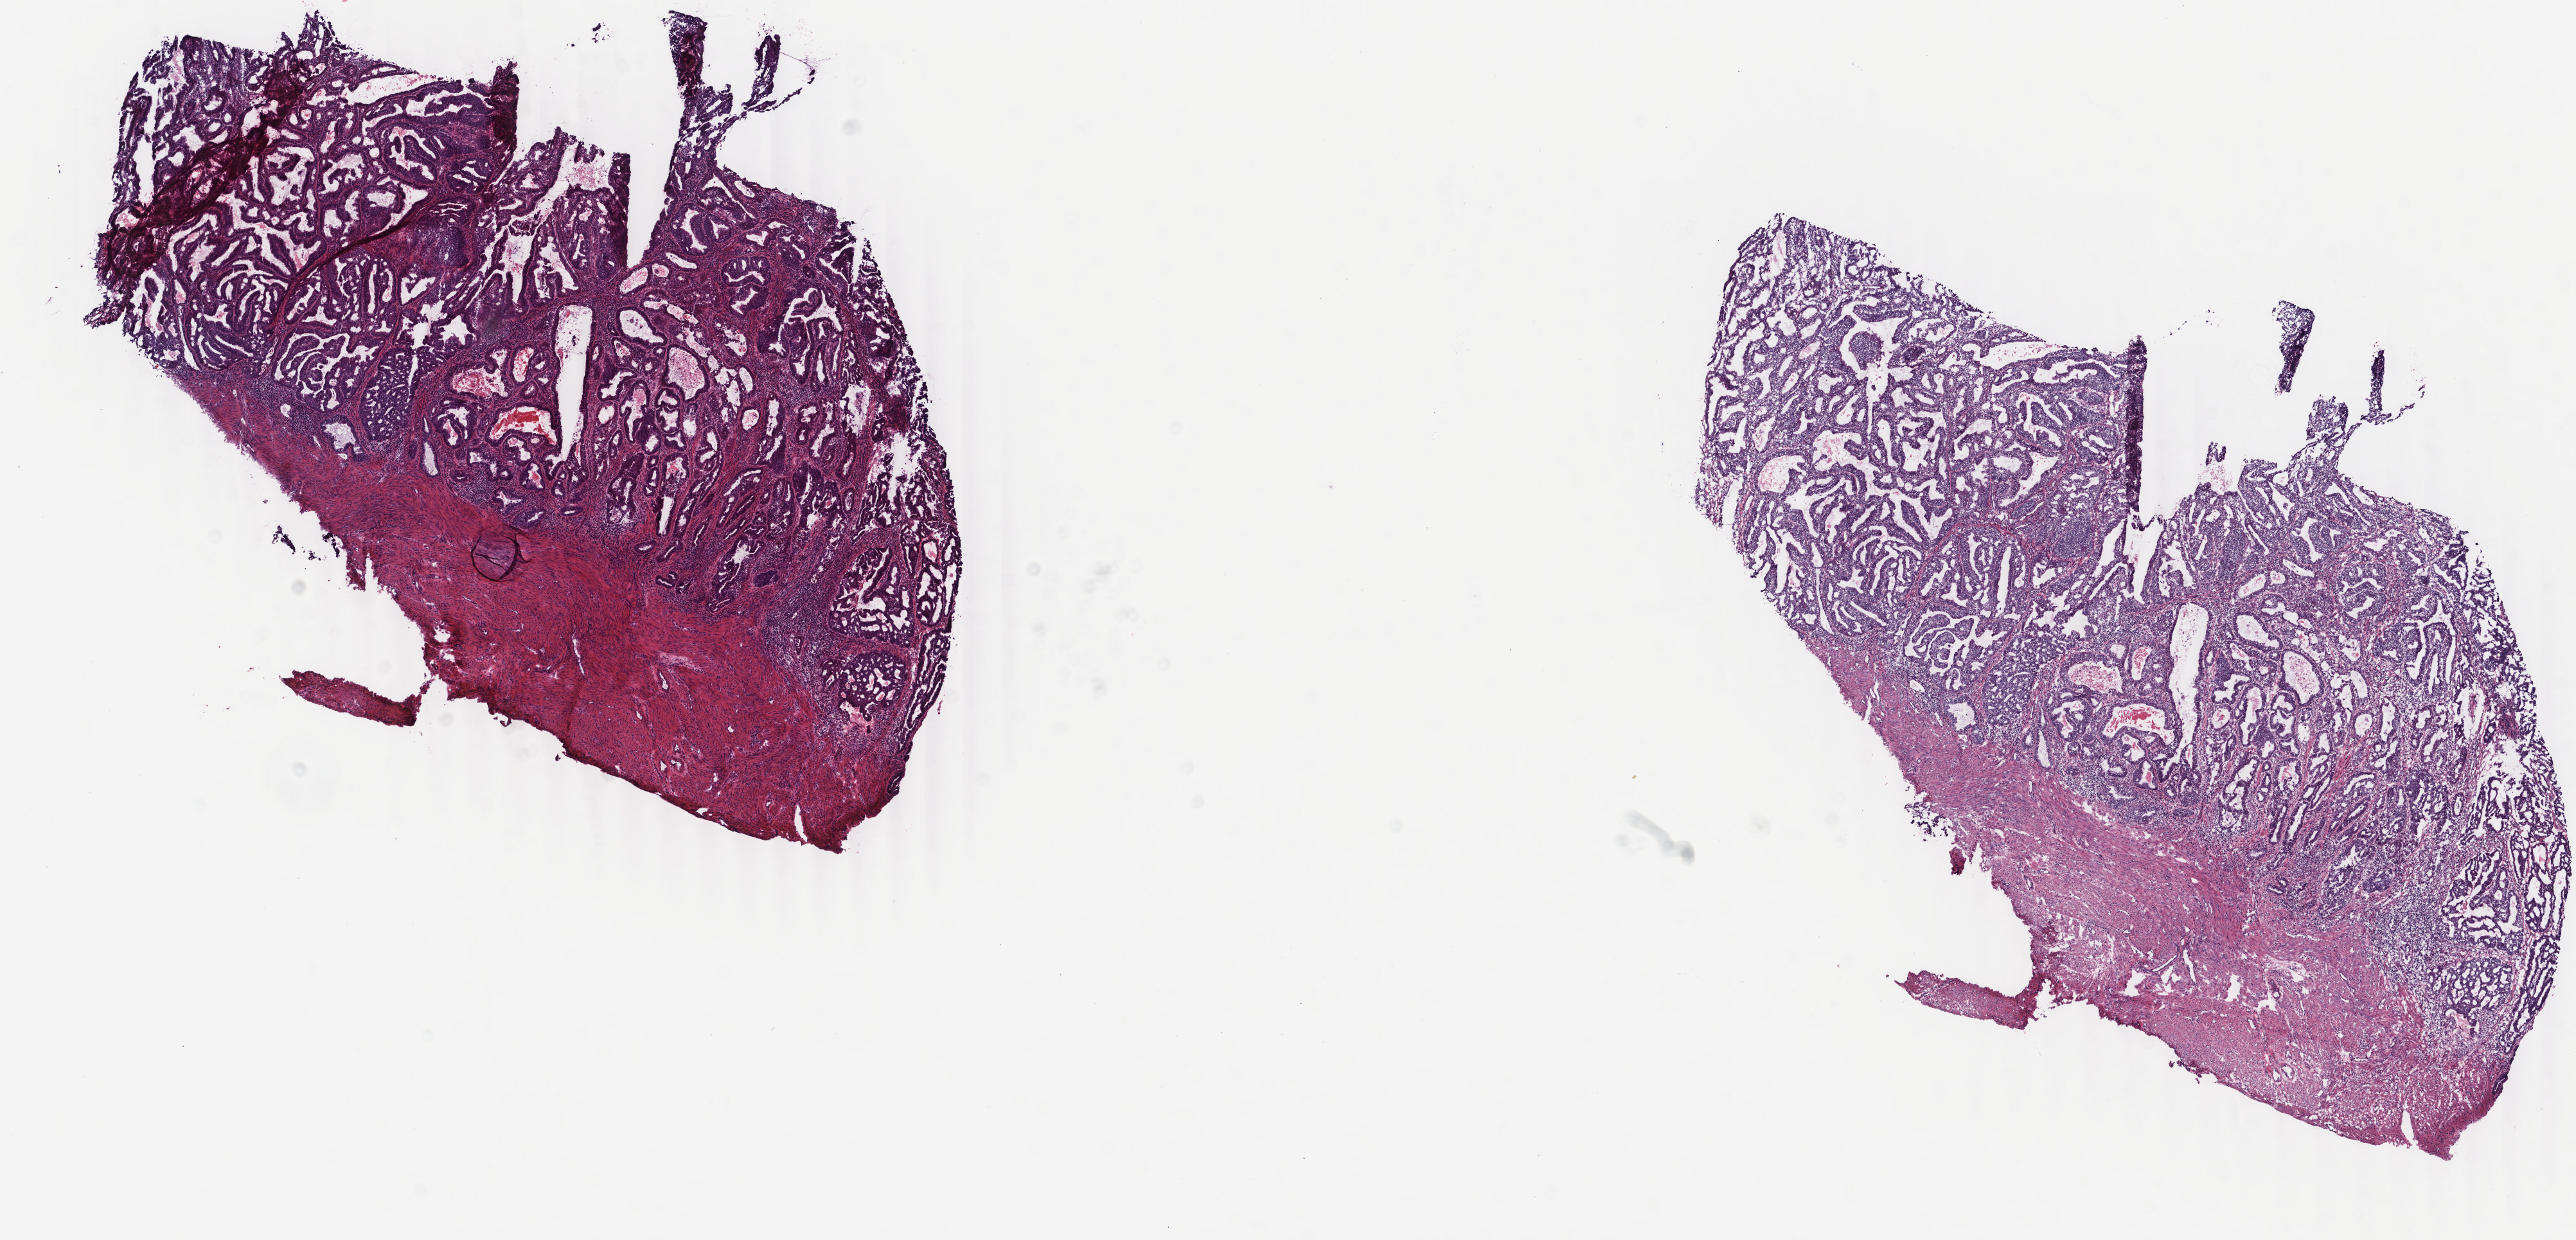
Digitized H&E-stained tissue section (whole slide), low-resolution overview of the scanned area, about 15.9 x 7.7 mm; frozen section; primary tumour sample from the uterus. Female patient; age at initial diagnosis 75 years. Histologic grade: G1 (well differentiated). Slide review estimates, as recorded: tumour cells 50%, tumour nuclei 60%, normal cells 30%, stromal cells 10%, necrosis 10%. Infiltration values recorded for this section: lymphocyte infiltration 20%, monocyte infiltration 0%, neutrophil infiltration 10%.
FIGO stage: IB. Histologic diagnosis: Endometrioid adenocarcinoma, NOS (endometrium).